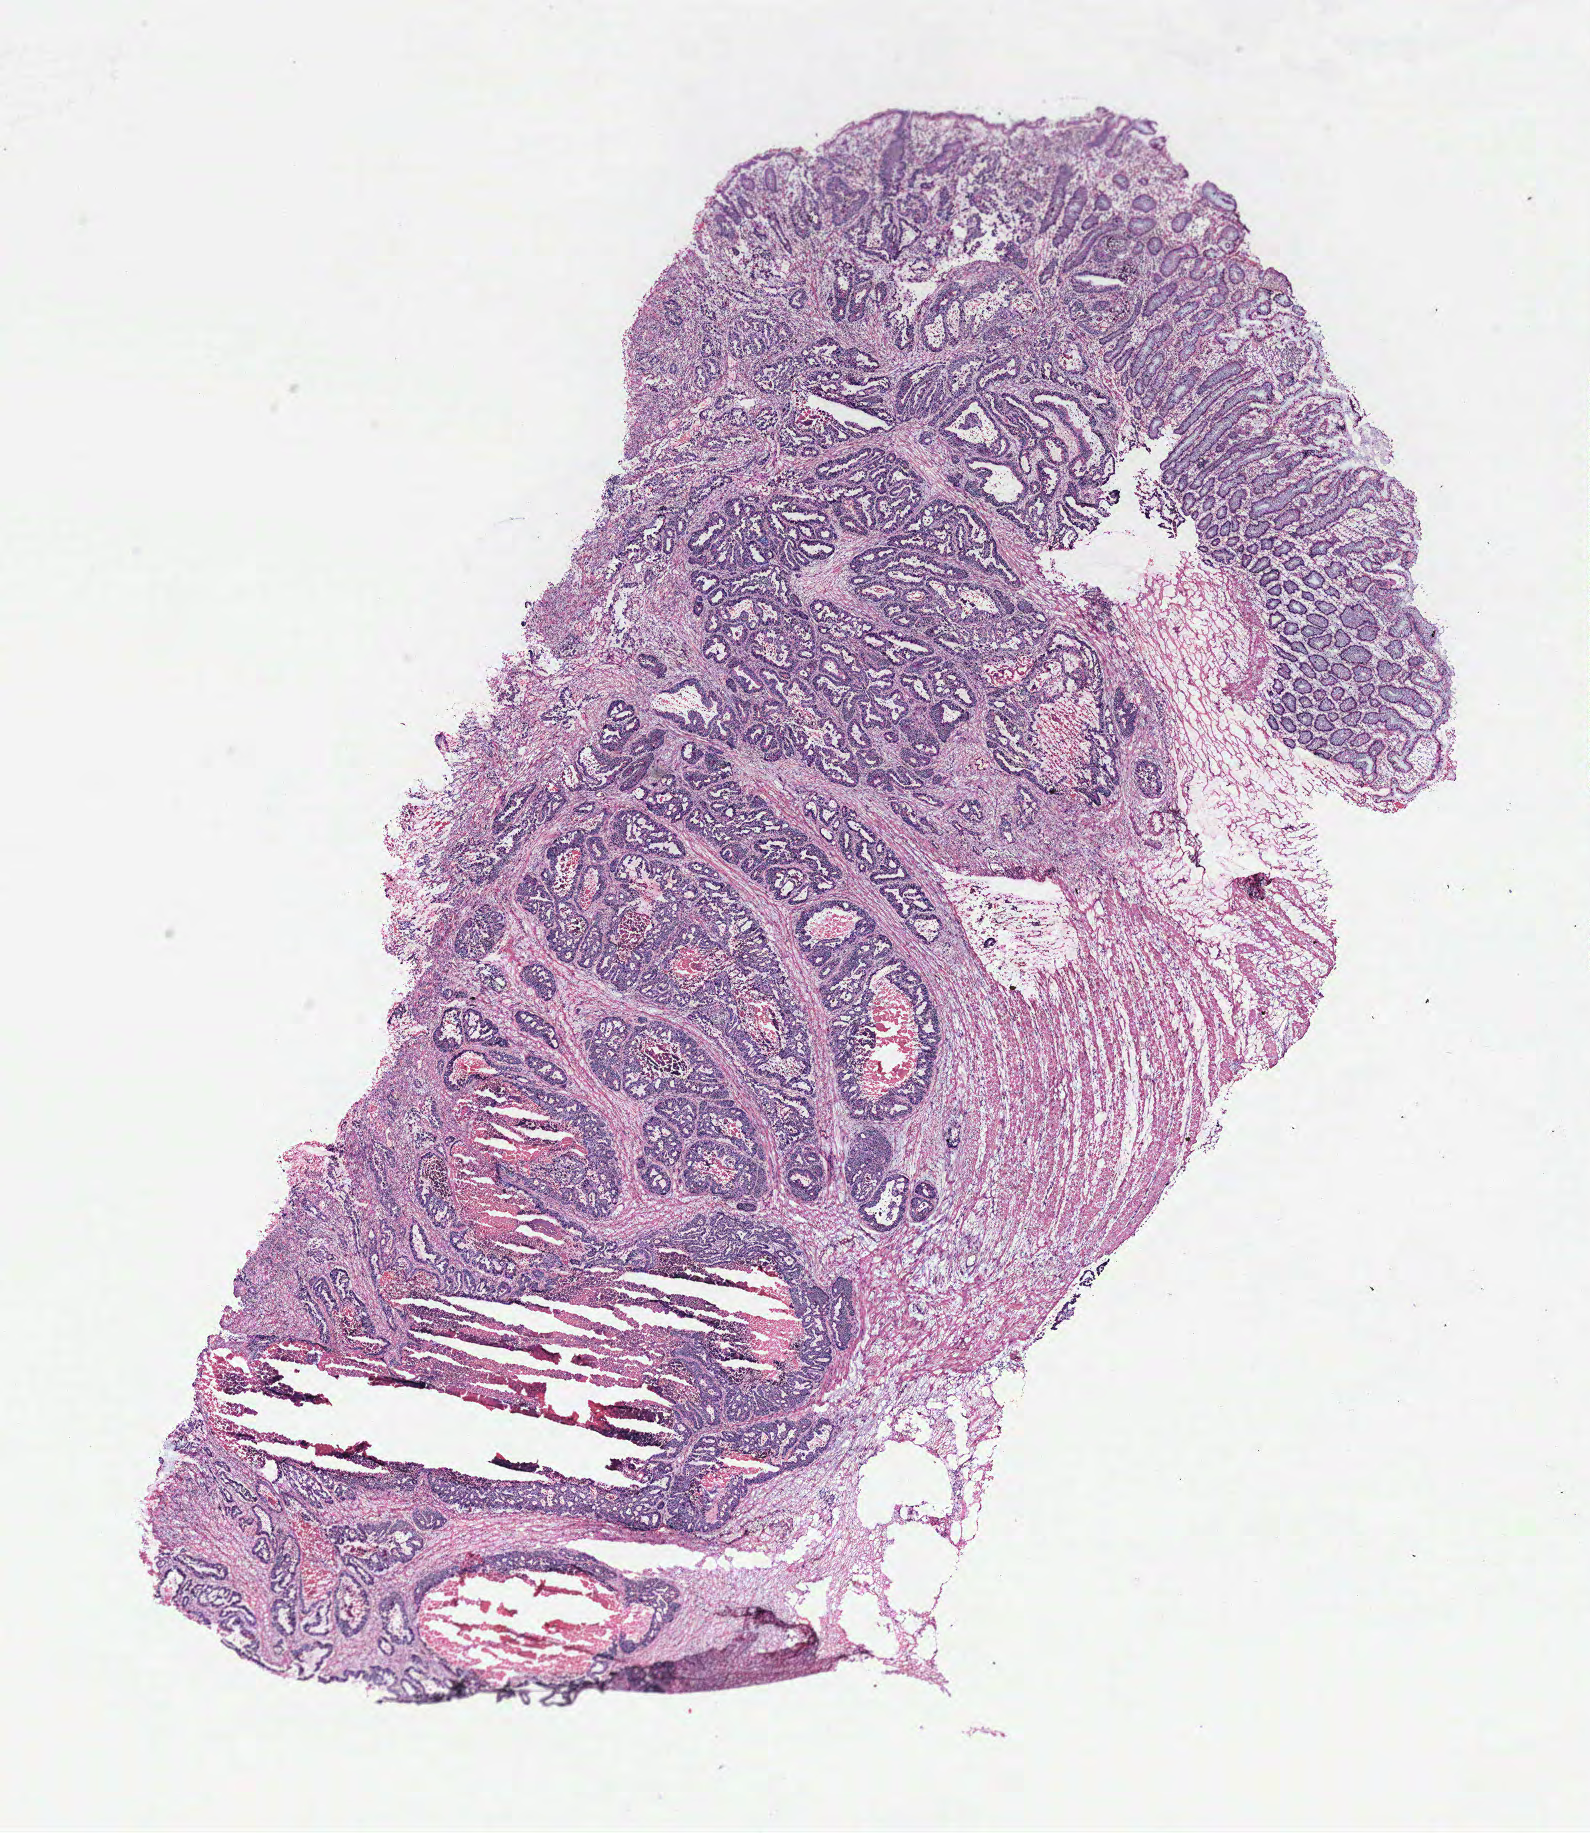
Digitized H&E tissue section (whole slide) — a low-resolution overview of the entire scanned area, about 12.7 x 14.7 mm; colon, normal (non-tumour) tissue. Female, 64 y/o.
This section: normal (non-tumour) tissue from the same patient. Patient diagnosis: Adenocarcinoma, NOS.